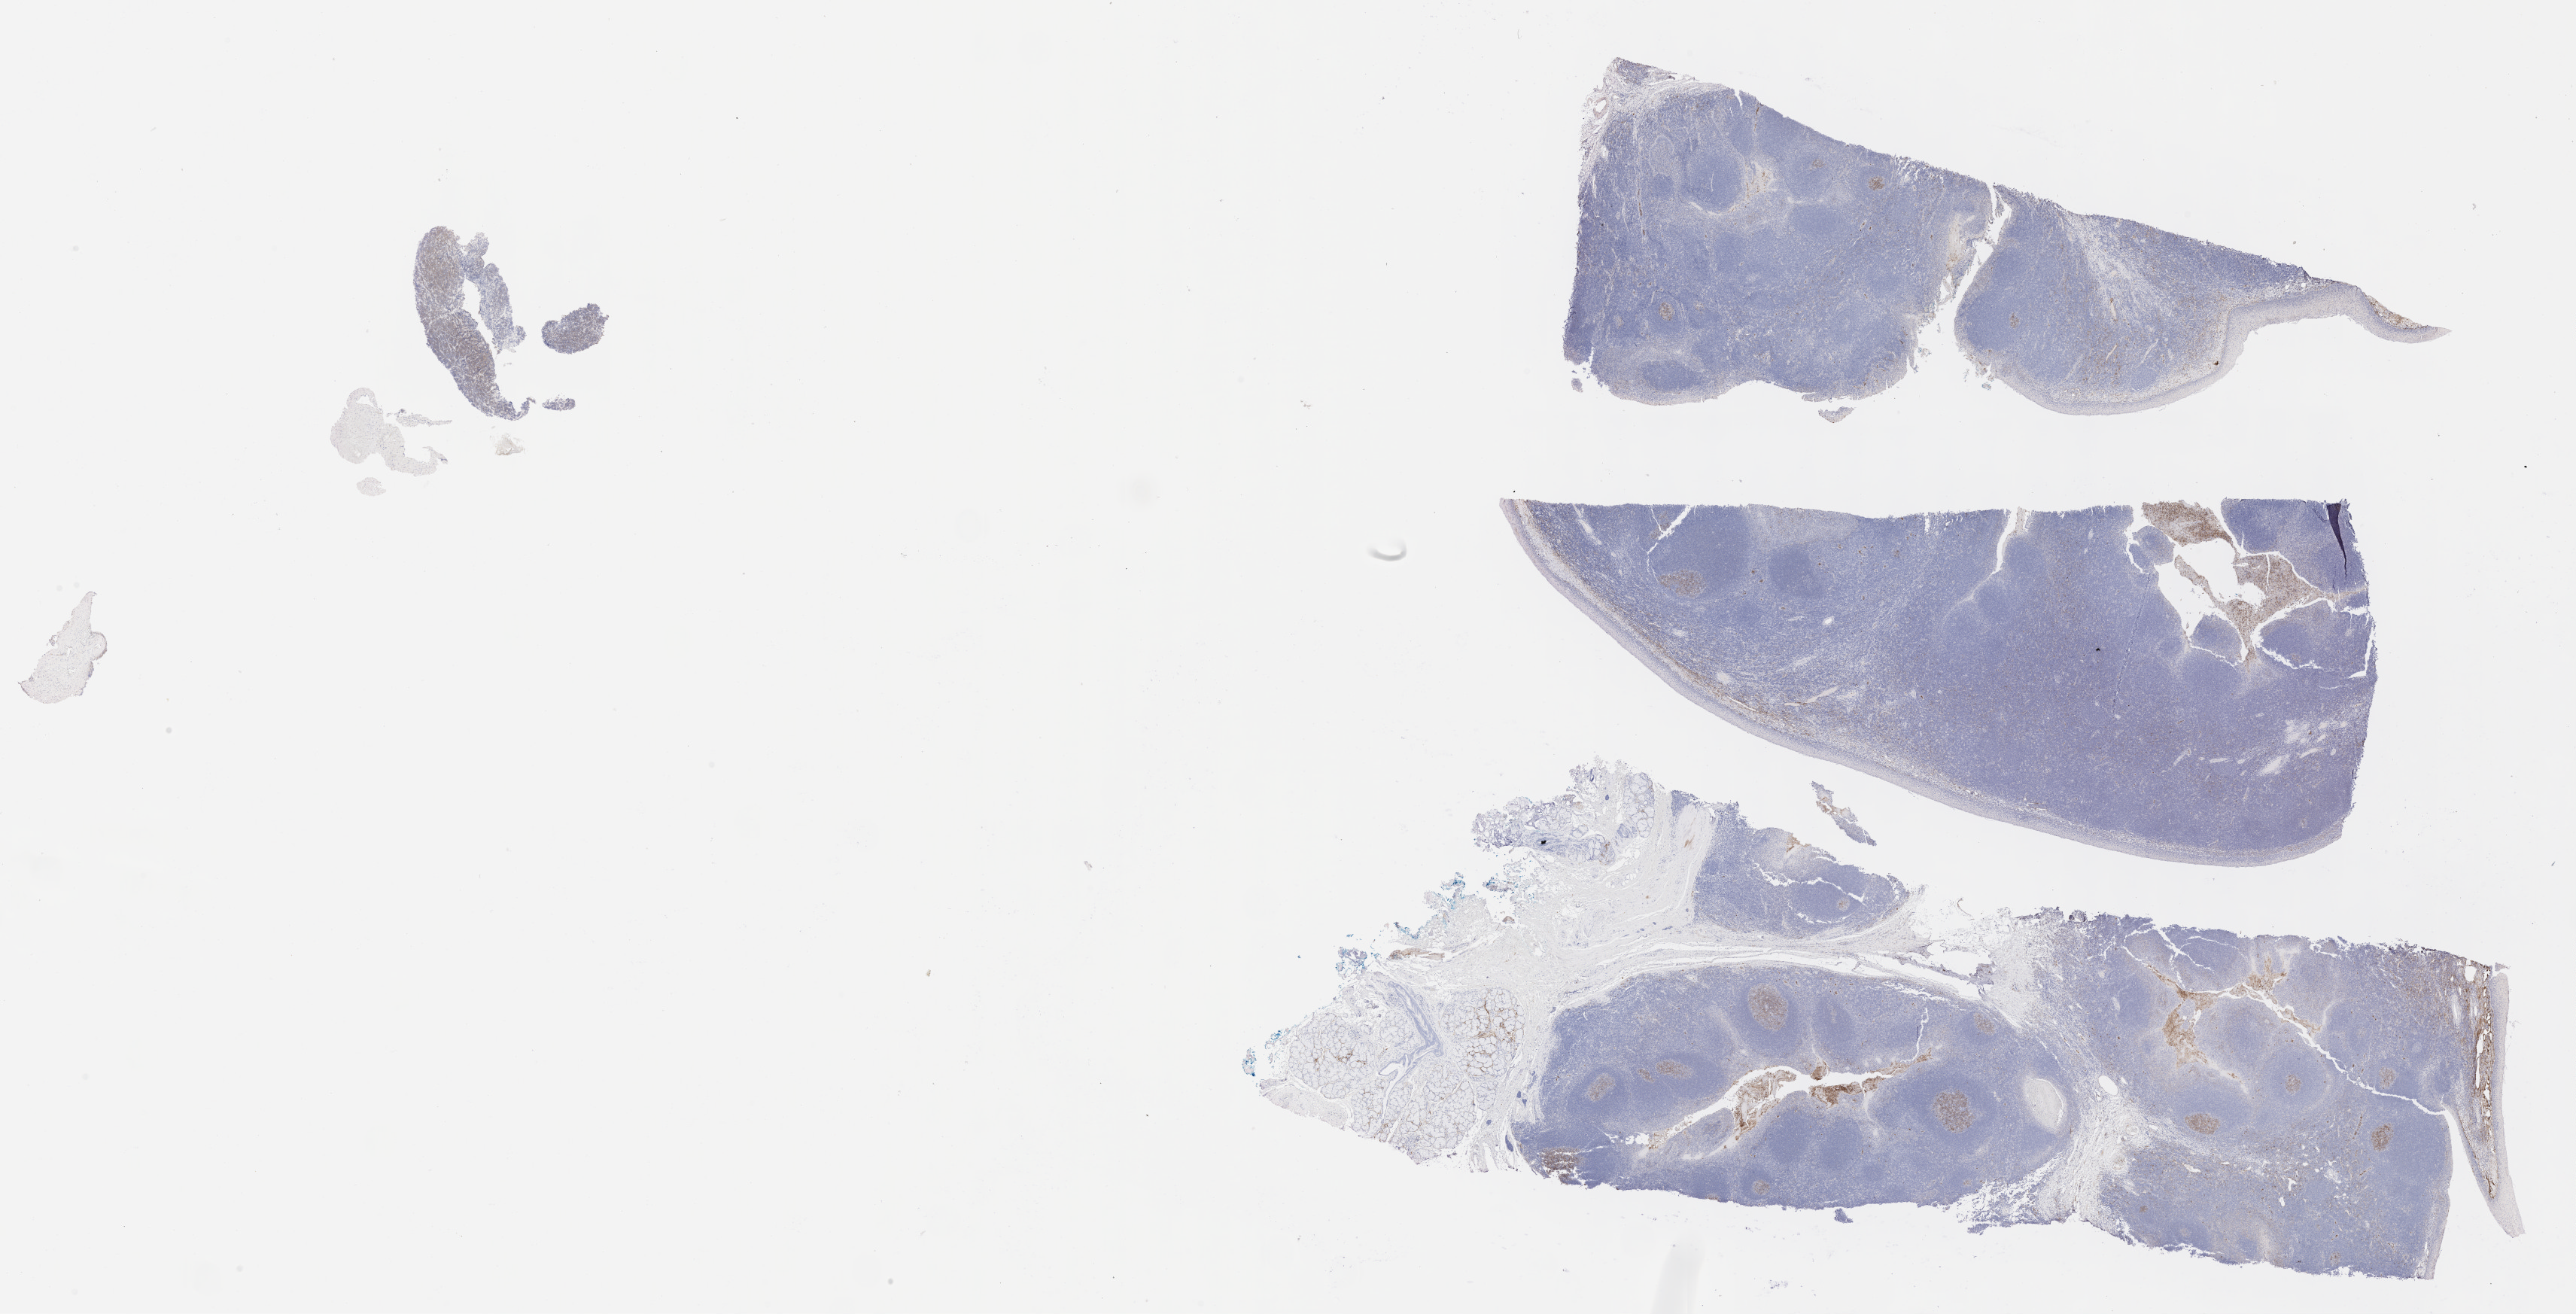
Immunohistochemistry (IHC) whole-slide image stained for CD10, a low-resolution overview of the entire scanned area, about 27.7 x 14.1 mm; specimen: tumor tissue; site: abdomen proper. Patient: female, age at initial diagnosis 7 years.
• histologic diagnosis: Burkitt lymphoma, NOS